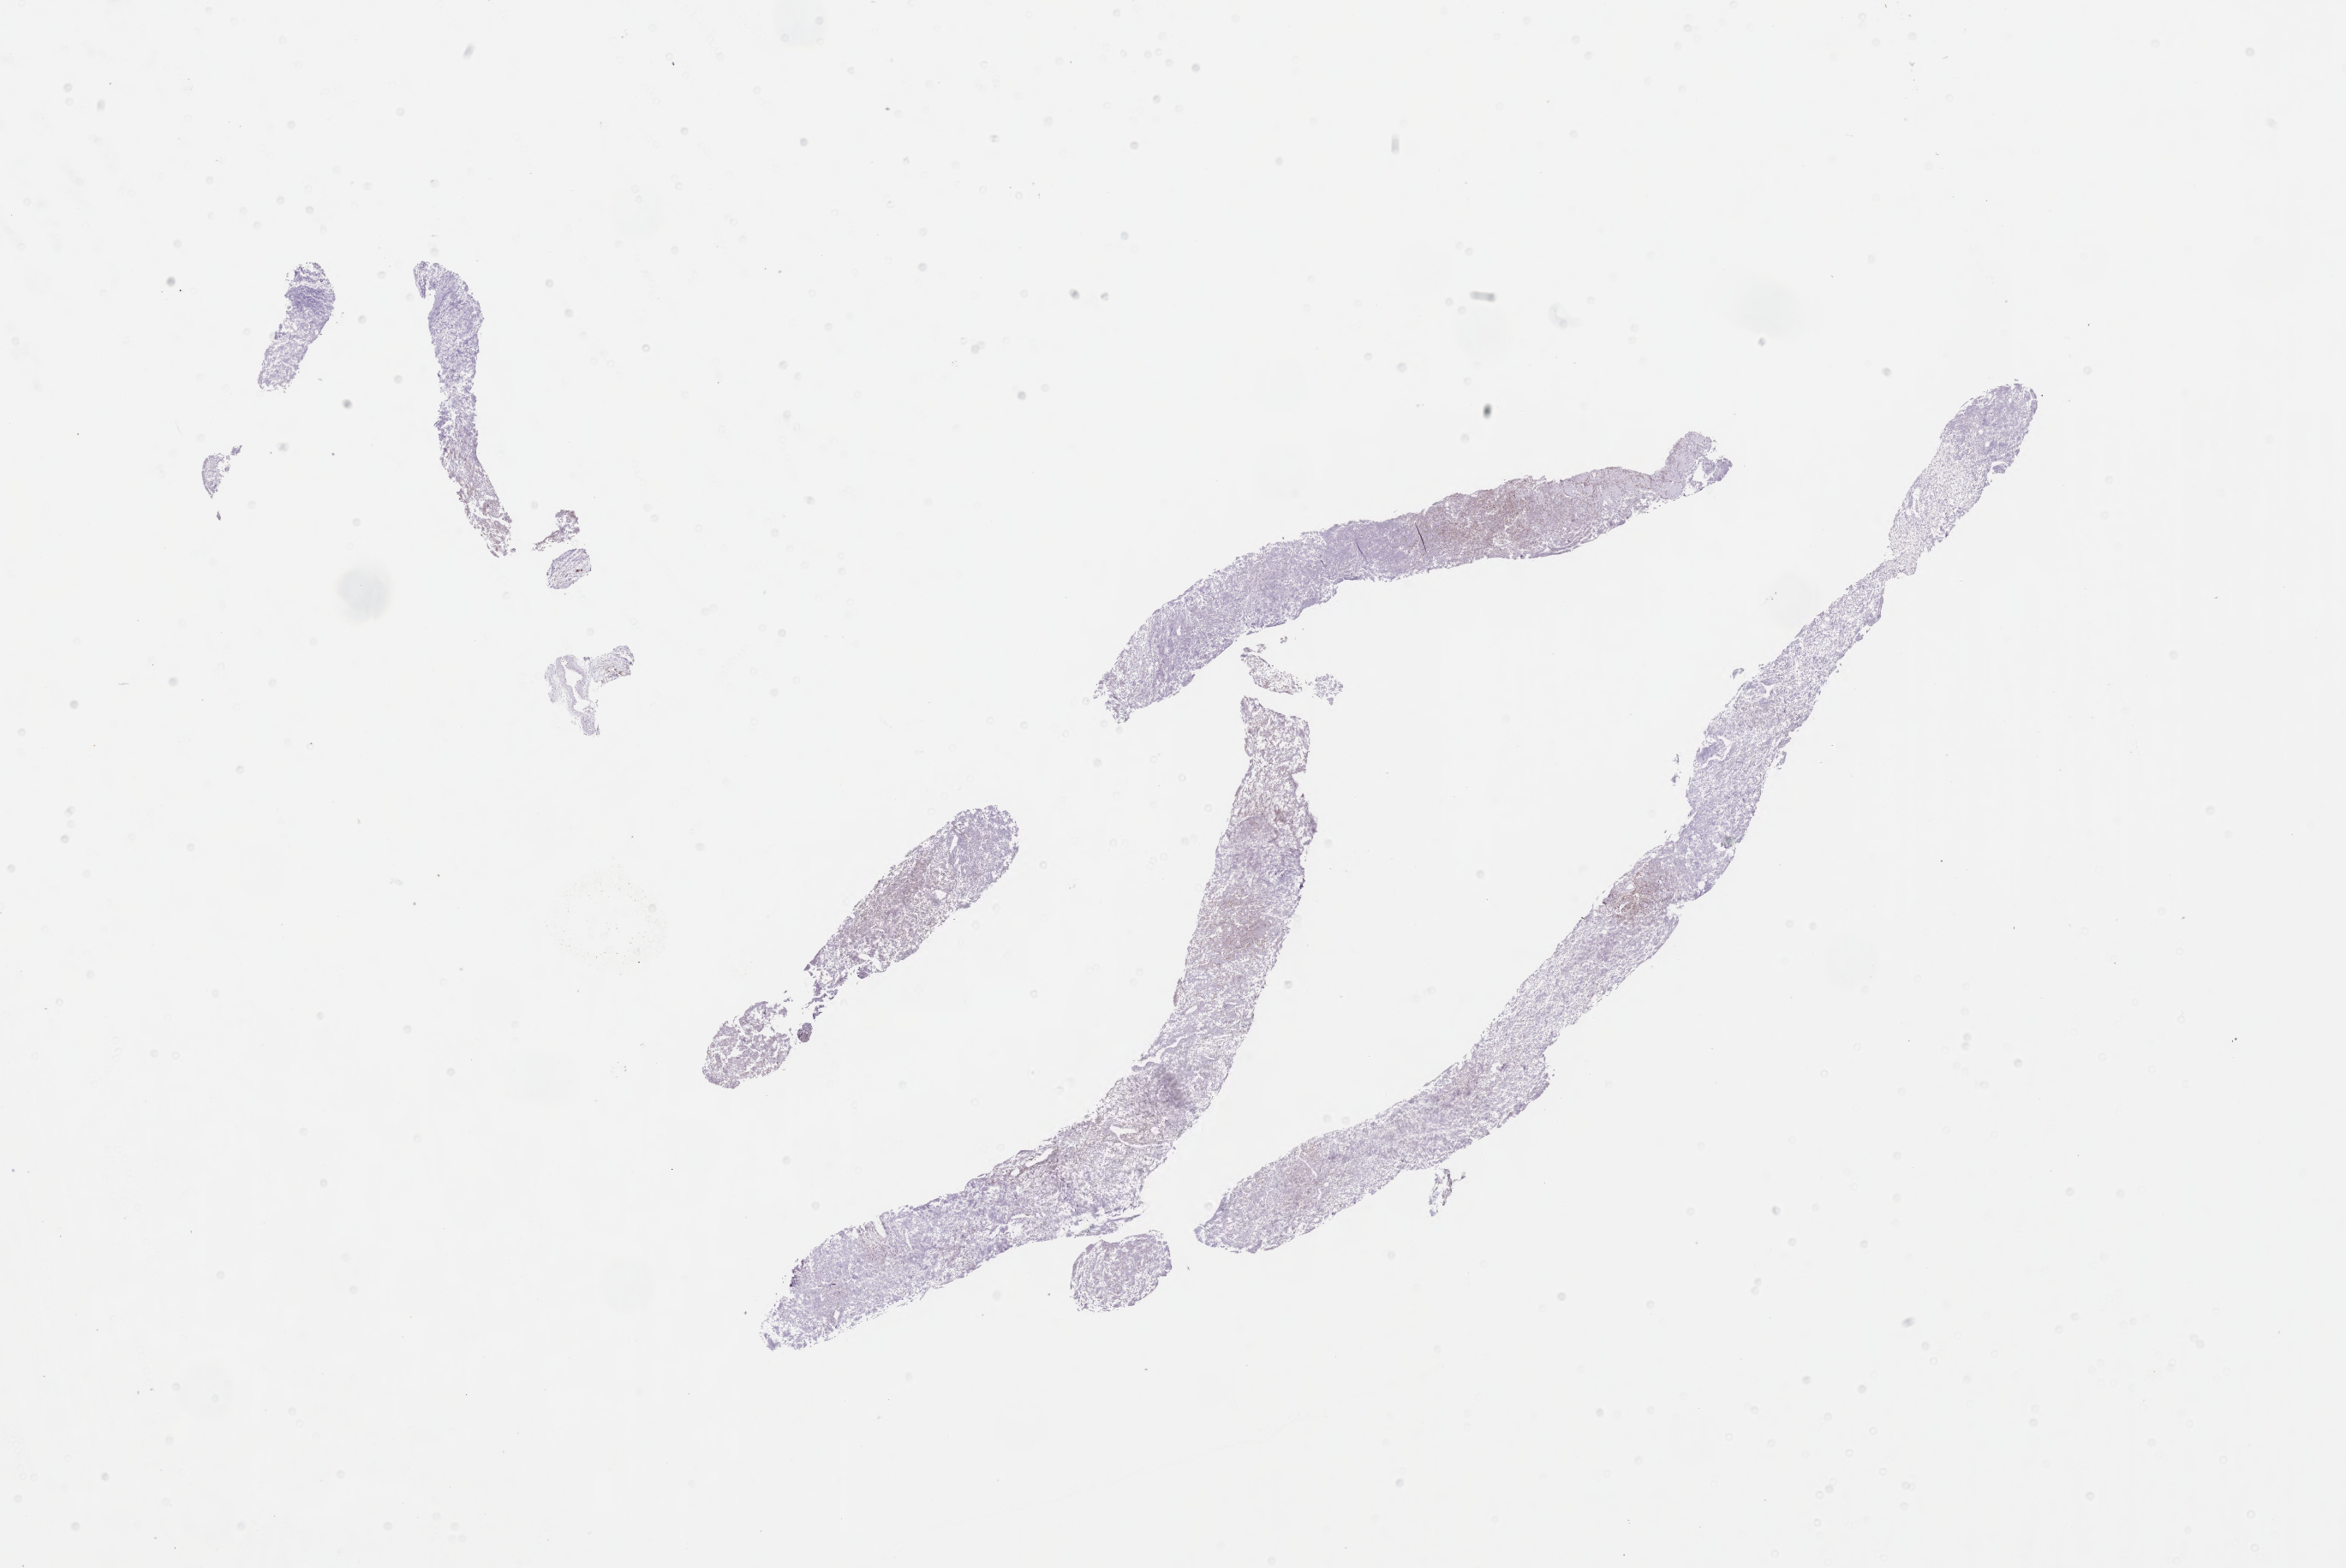
IHC for BCL6, whole-slide image, low-resolution overview of the scanned area, about 22.1 x 14.8 mm. Tumor tissue. Patient male; 66 years old.
- diagnosis: Burkitt lymphoma, NOS